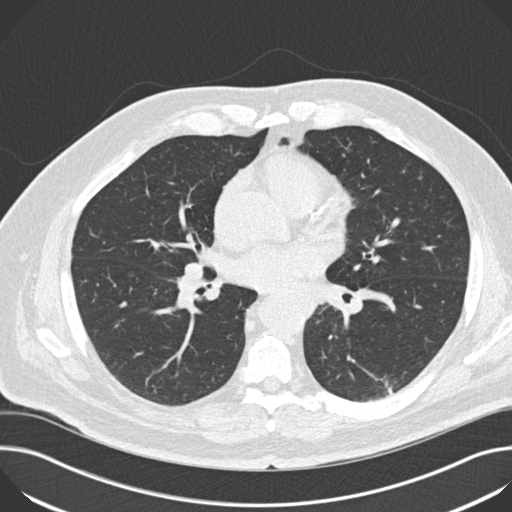
Chest CT (low-dose screening protocol), one axial image; third screening round (two years after baseline); lung window (W 1500 / L -600 HU); standard (soft-tissue) reconstruction kernel (B30f); 512 × 512 image matrix. Male participant, aged 68 years at enrolment.
• Expert reader's lesion annotation, box from (x=158, y=235) to (x=233, y=307) px.
• No non-calcified nodule or mass ≥4 mm was recorded by the screening reader at this exam.
• Official screen result: negative screen, no significant abnormalities.
• Participant outcome: lung cancer diagnosed 151 days after this screen — small cell carcinoma, NOS, right hilum, mediastinum, stage IV (AJCC 6th edition).